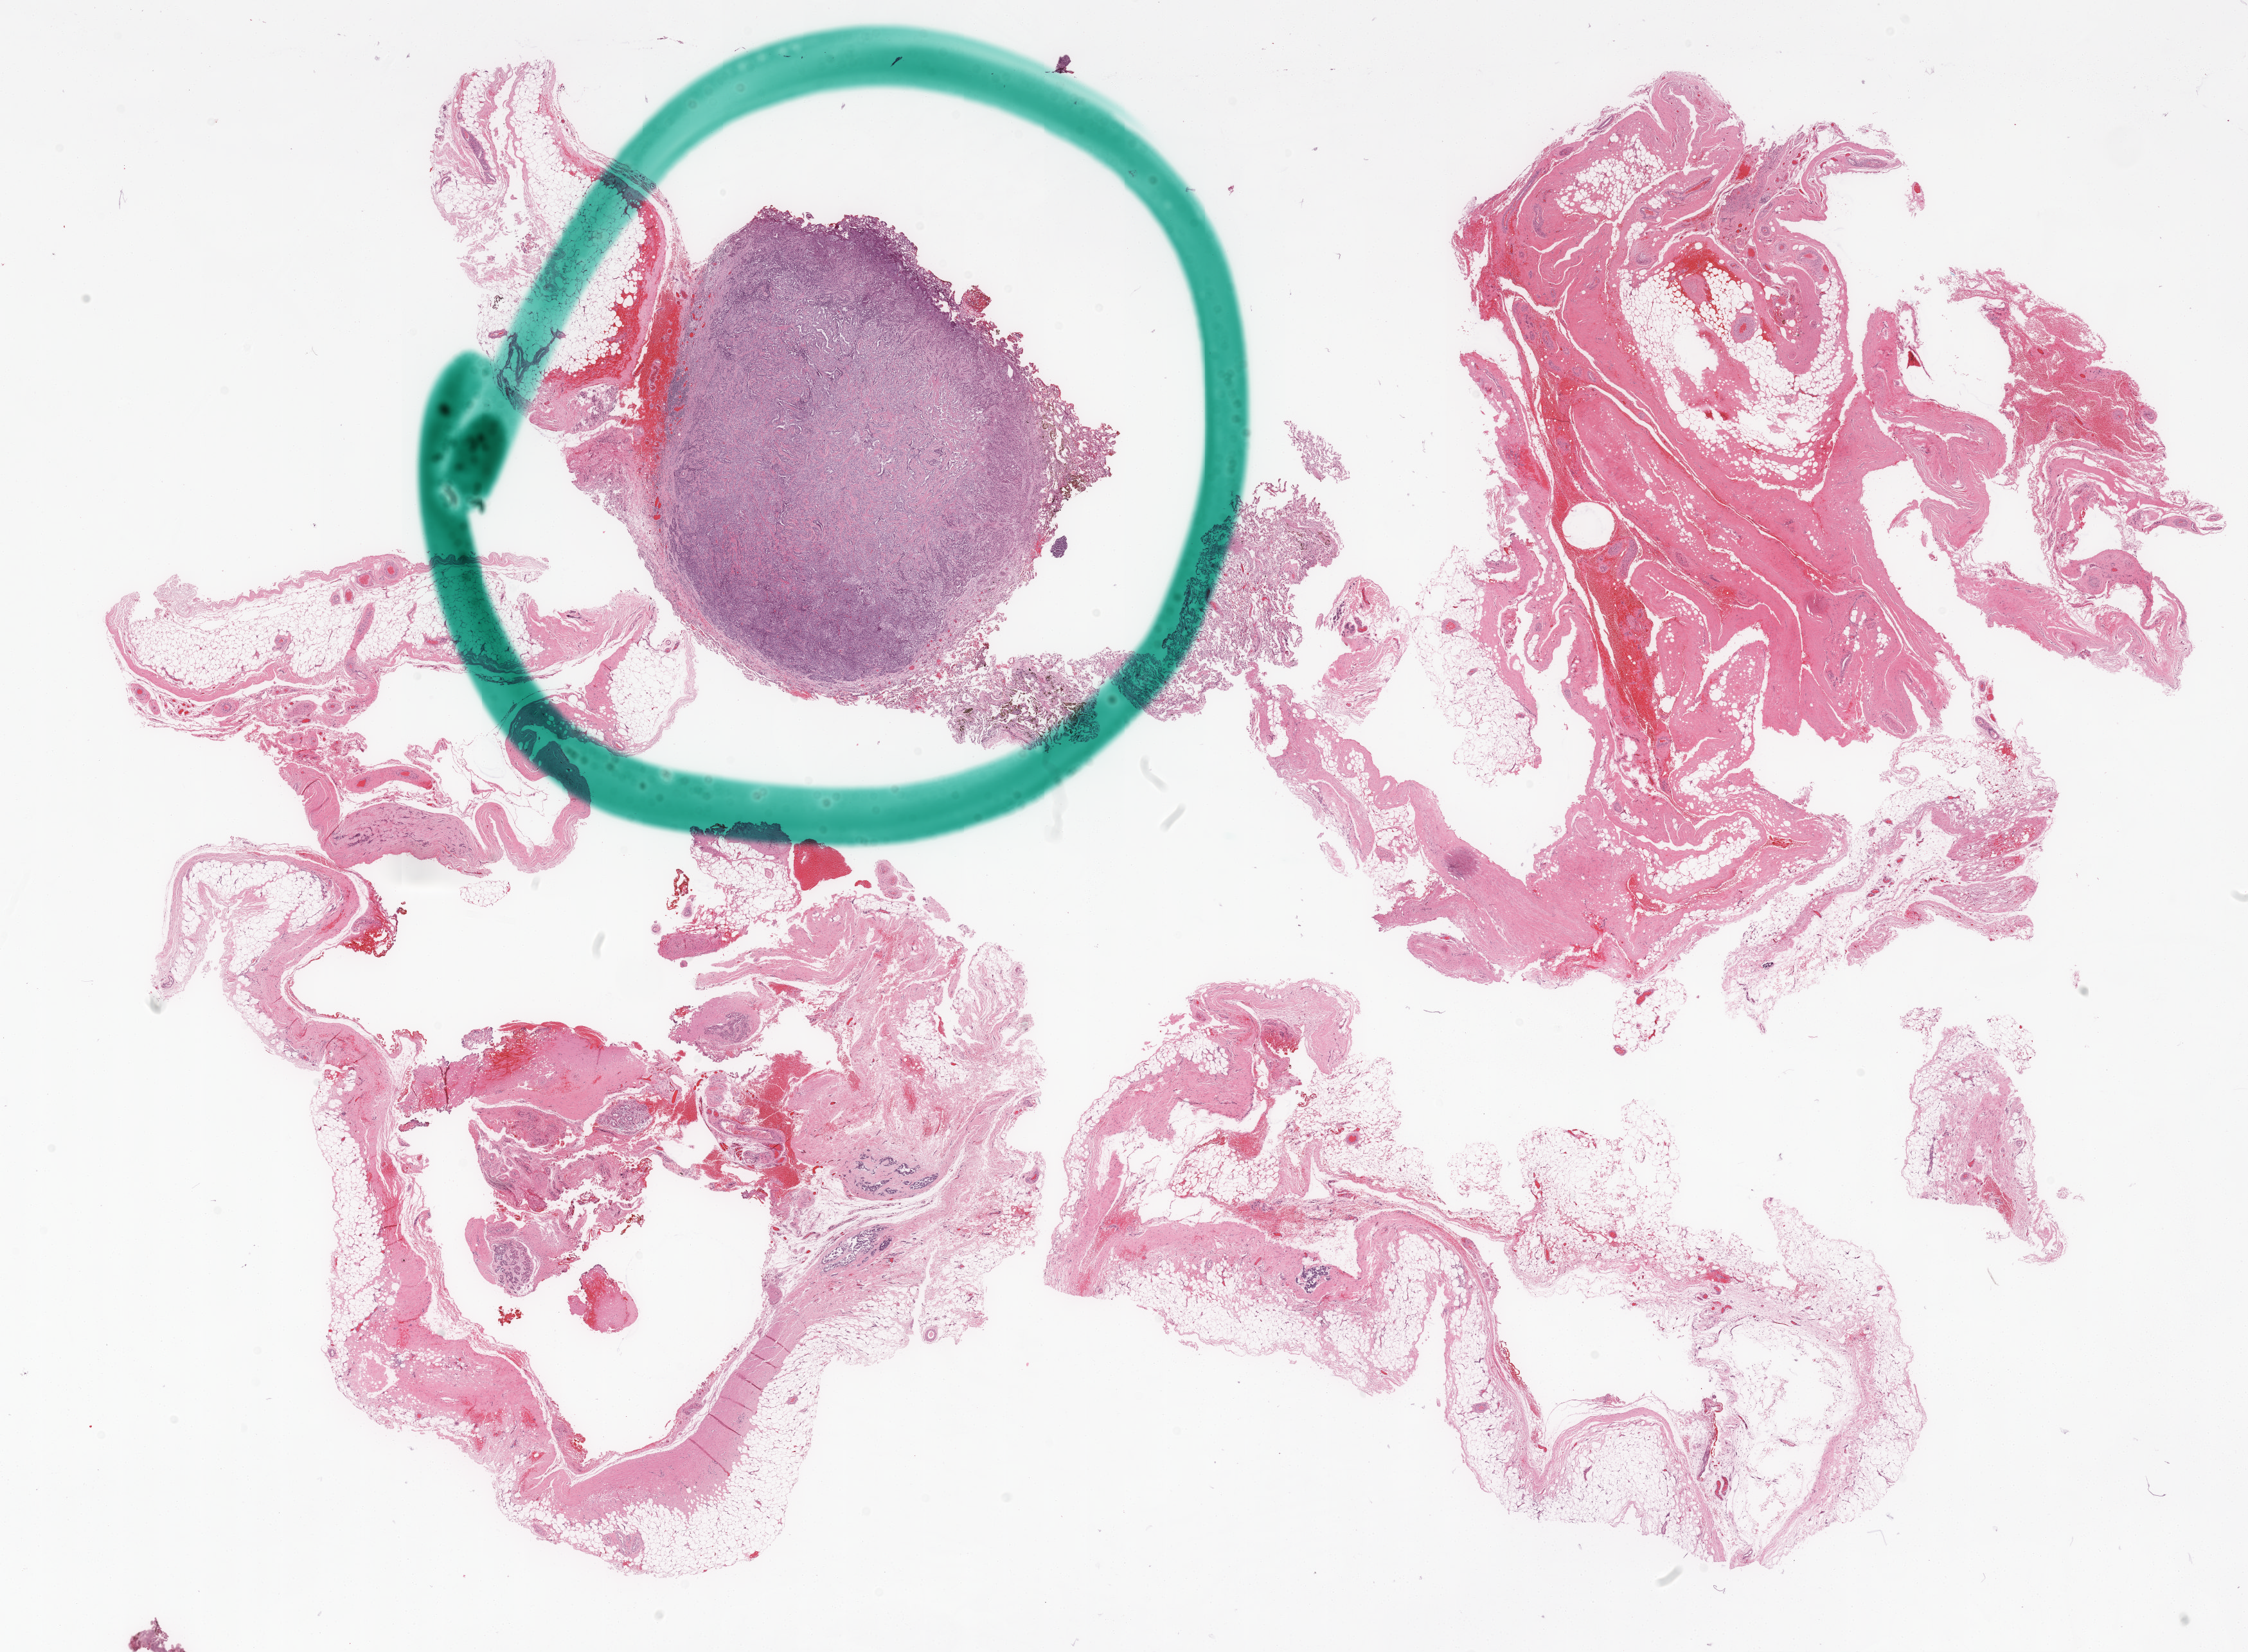
Digitized H&E tissue section (whole slide) — a low-resolution overview of the entire scanned area, about 28.1 x 20.6 mm (acquisition: 20x scan). FFPE section. Sample: primary tumour, mesothelium. Patient: male, age at initial diagnosis 73 years.
TNM: T1b N2 M0. AJCC pathologic stage: III (7th edition). Diagnosis: Epithelioid mesothelioma, malignant (pleura, NOS).